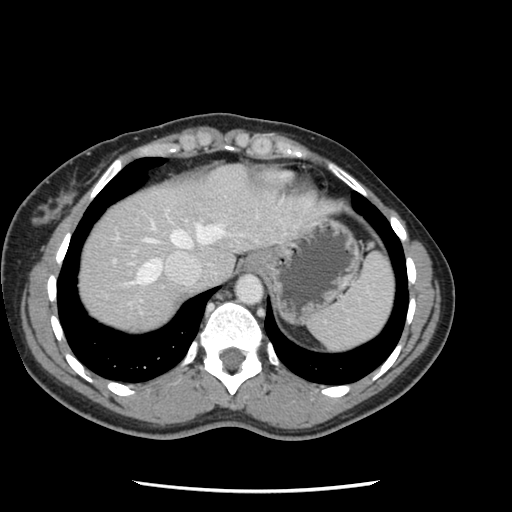
Contrast-enhanced abdominal CT, one axial slice. Slice 104 of 134 in the series (ordered by position). 120 kVp. Intravenous contrast given. Soft-tissue window (W 400 / L 40 HU). 512 × 512 image matrix. Female patient, age 43 years. From the clinical record (not read from this slice): diagnosis: colorectal cancer liver metastases, imaged before liver resection; multiple liver metastases: yes.
Structures marked on this image (outlined manually by an expert reader):
- hepatic veins: box from (x=133, y=223) to (x=226, y=285) px
- liver: (x=79, y=166)–(x=301, y=329)
- planned liver remnant (the part of the liver to remain after resection): (x=79, y=184)–(x=200, y=304)
- portal vein (with intrahepatic branches): (x=113, y=236)–(x=136, y=263)